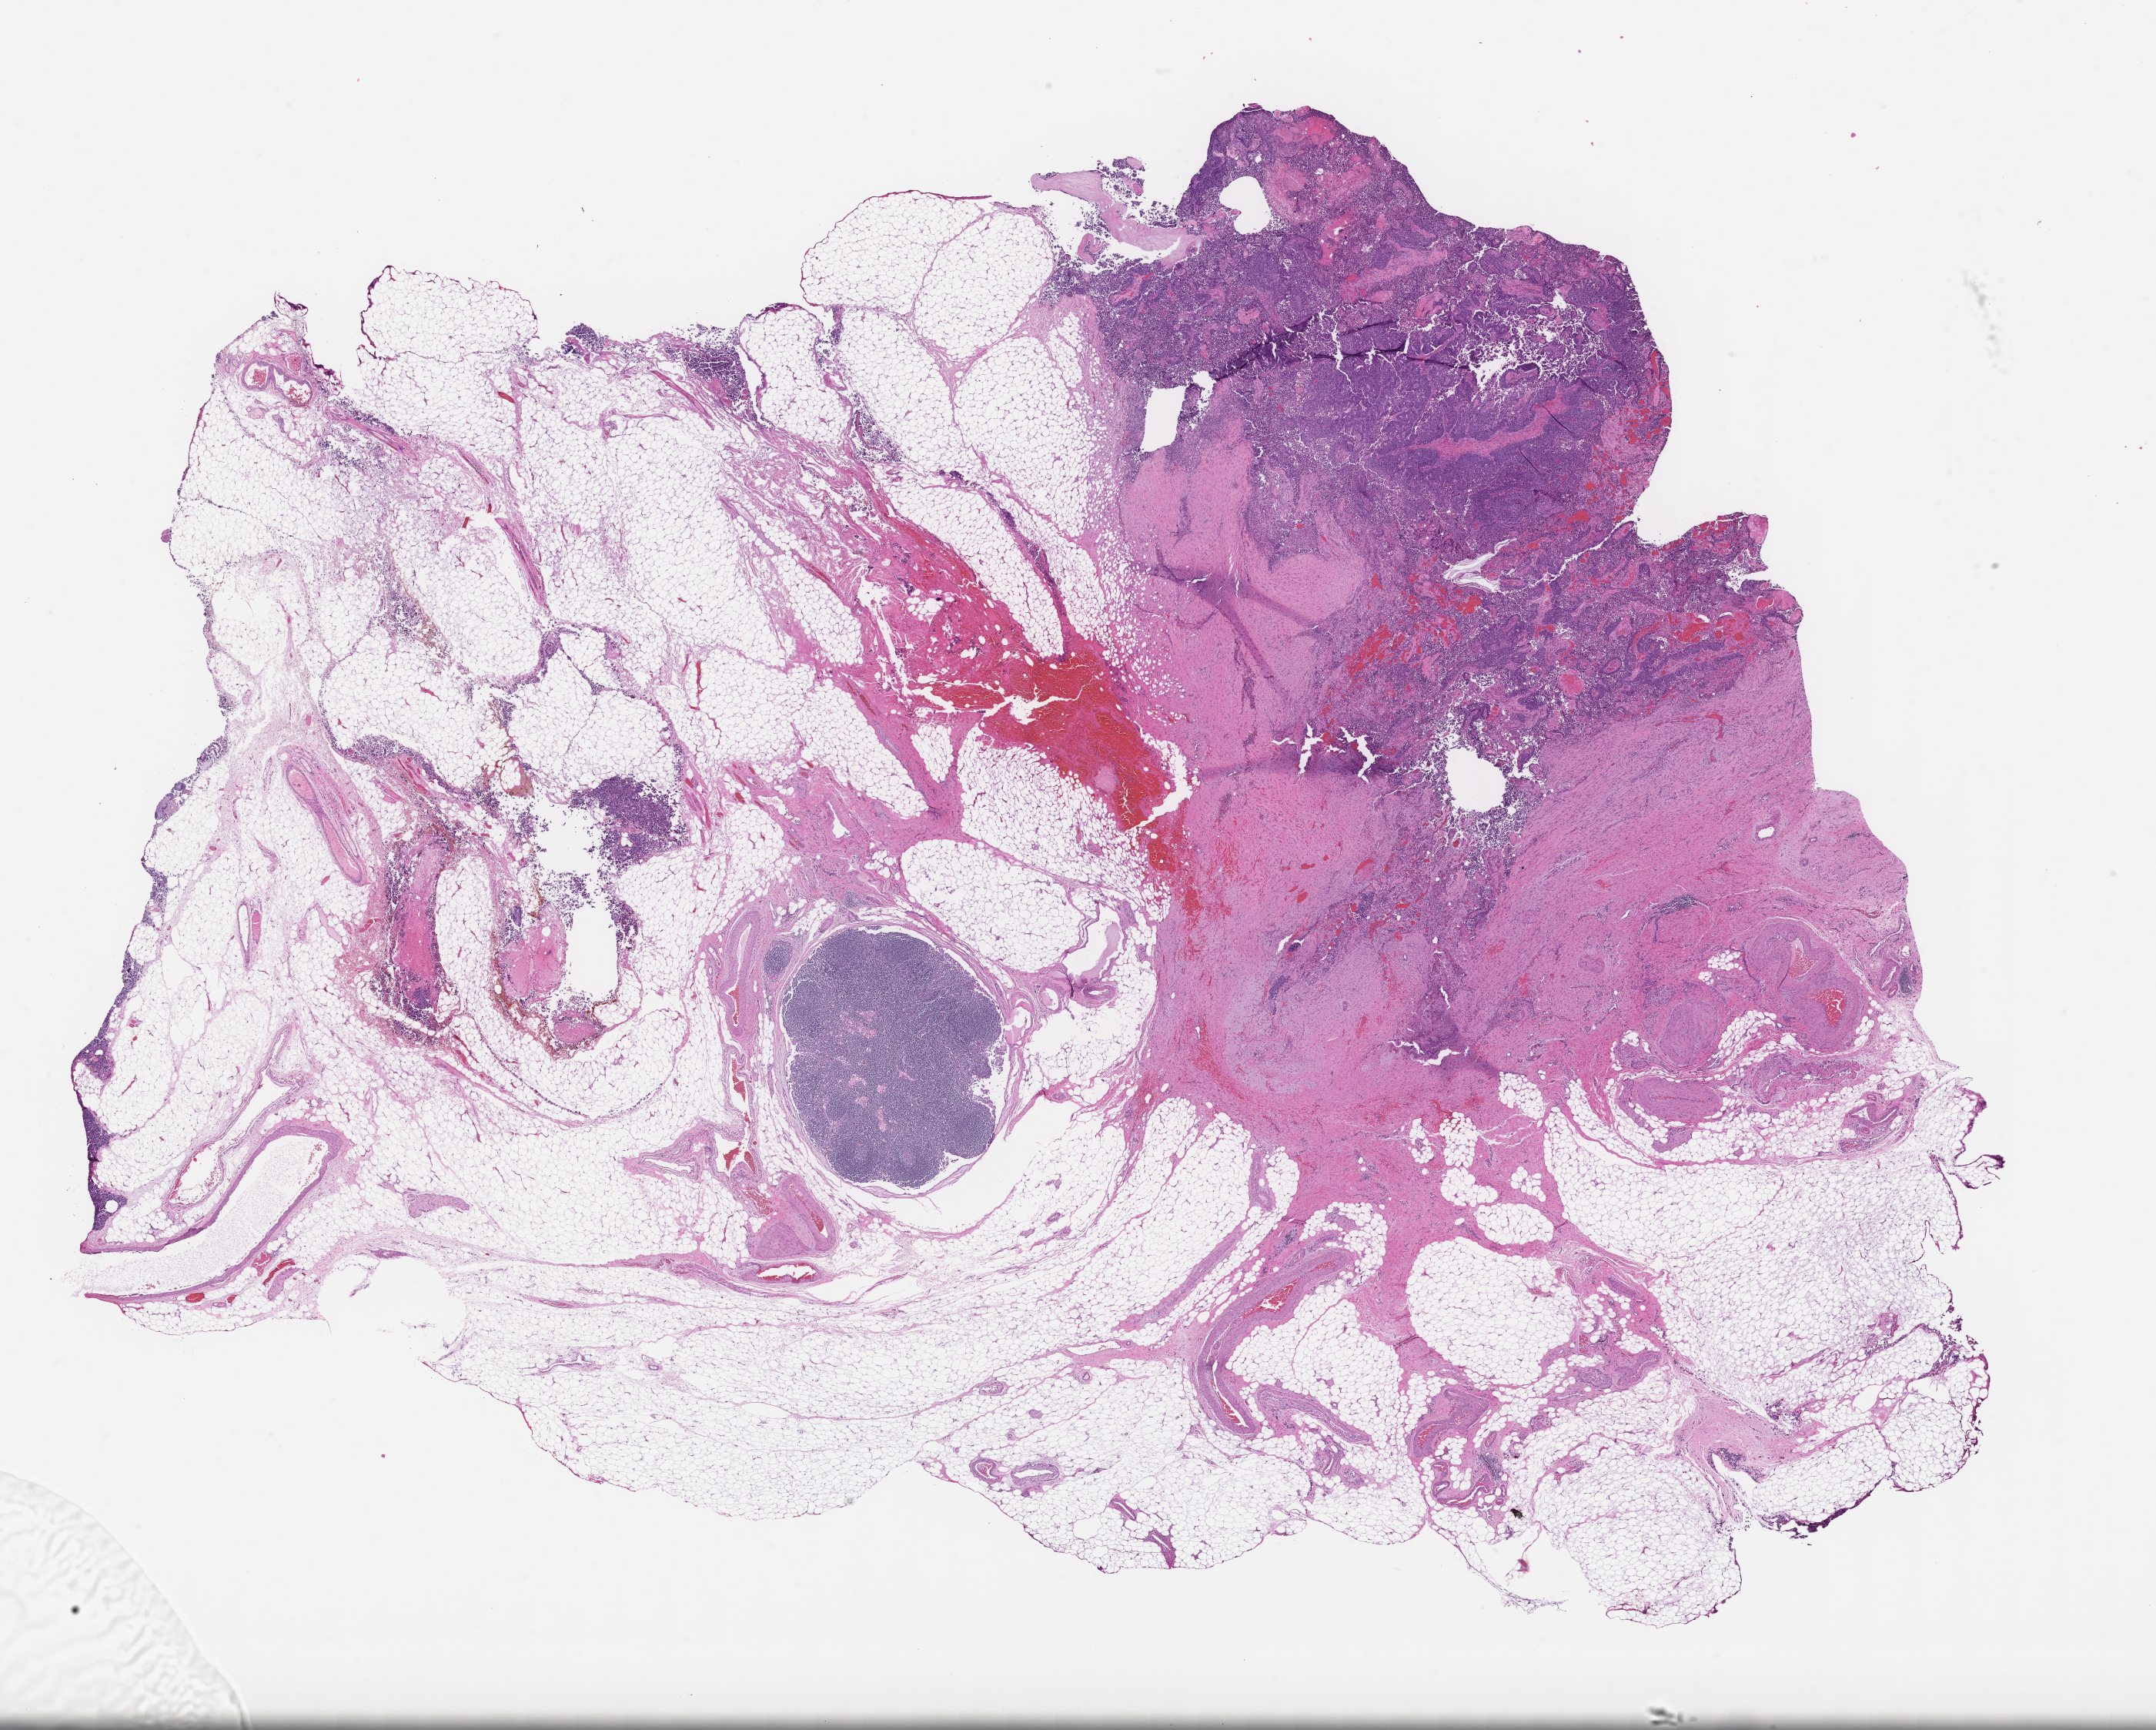
Whole-slide image, haematoxylin and eosin stain, shown as a low-resolution overview of the whole scanned area (about 22.6 x 18.1 mm); formalin-fixed, paraffin-embedded (FFPE) tissue; archival tissue. Female patient.
This section: metastasis (sampled organ not recorded). Primary diagnosis of the patient: Ovarian Carcinoma.